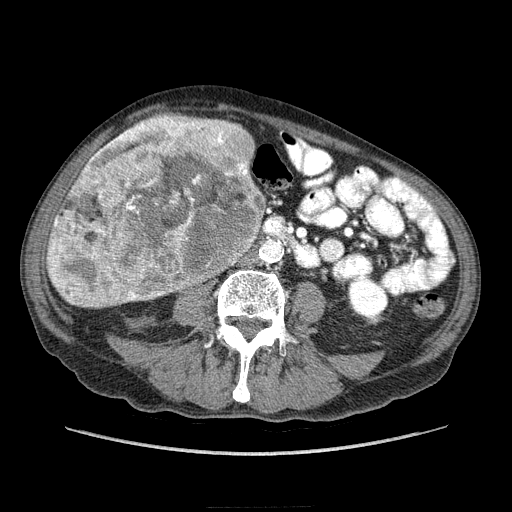
Contrast-enhanced abdominal CT (liver protocol), one axial slice. Position 59 of 218 along the scan axis. Reconstruction kernel STANDARD. 100 kVp. Soft-tissue window (W 400 / L 40 HU). 2.5 mm slice thickness. 512 × 512 image matrix, field of view 380 × 380 mm. Case-level facts recorded for this patient, not image findings: diagnosis: hepatocellular carcinoma (patient treated with transarterial chemoembolisation; whether this scan precedes or follows treatment is not stated here); TNM stage (as recorded): Stage-IIIA; Child-Pugh class: A; tumour differentiation: well differentiated; tumour nodularity: multinodular.
Annotated regions visible in this slice (semi-automatically segmented with operator editing):
- liver parenchyma outside the tumour (the mass and vessels are separate outlines, so this box may not span the whole liver): bounding box [x1, y1, x2, y2] px = [48, 118, 254, 306]
- mass: [48, 114, 264, 309]